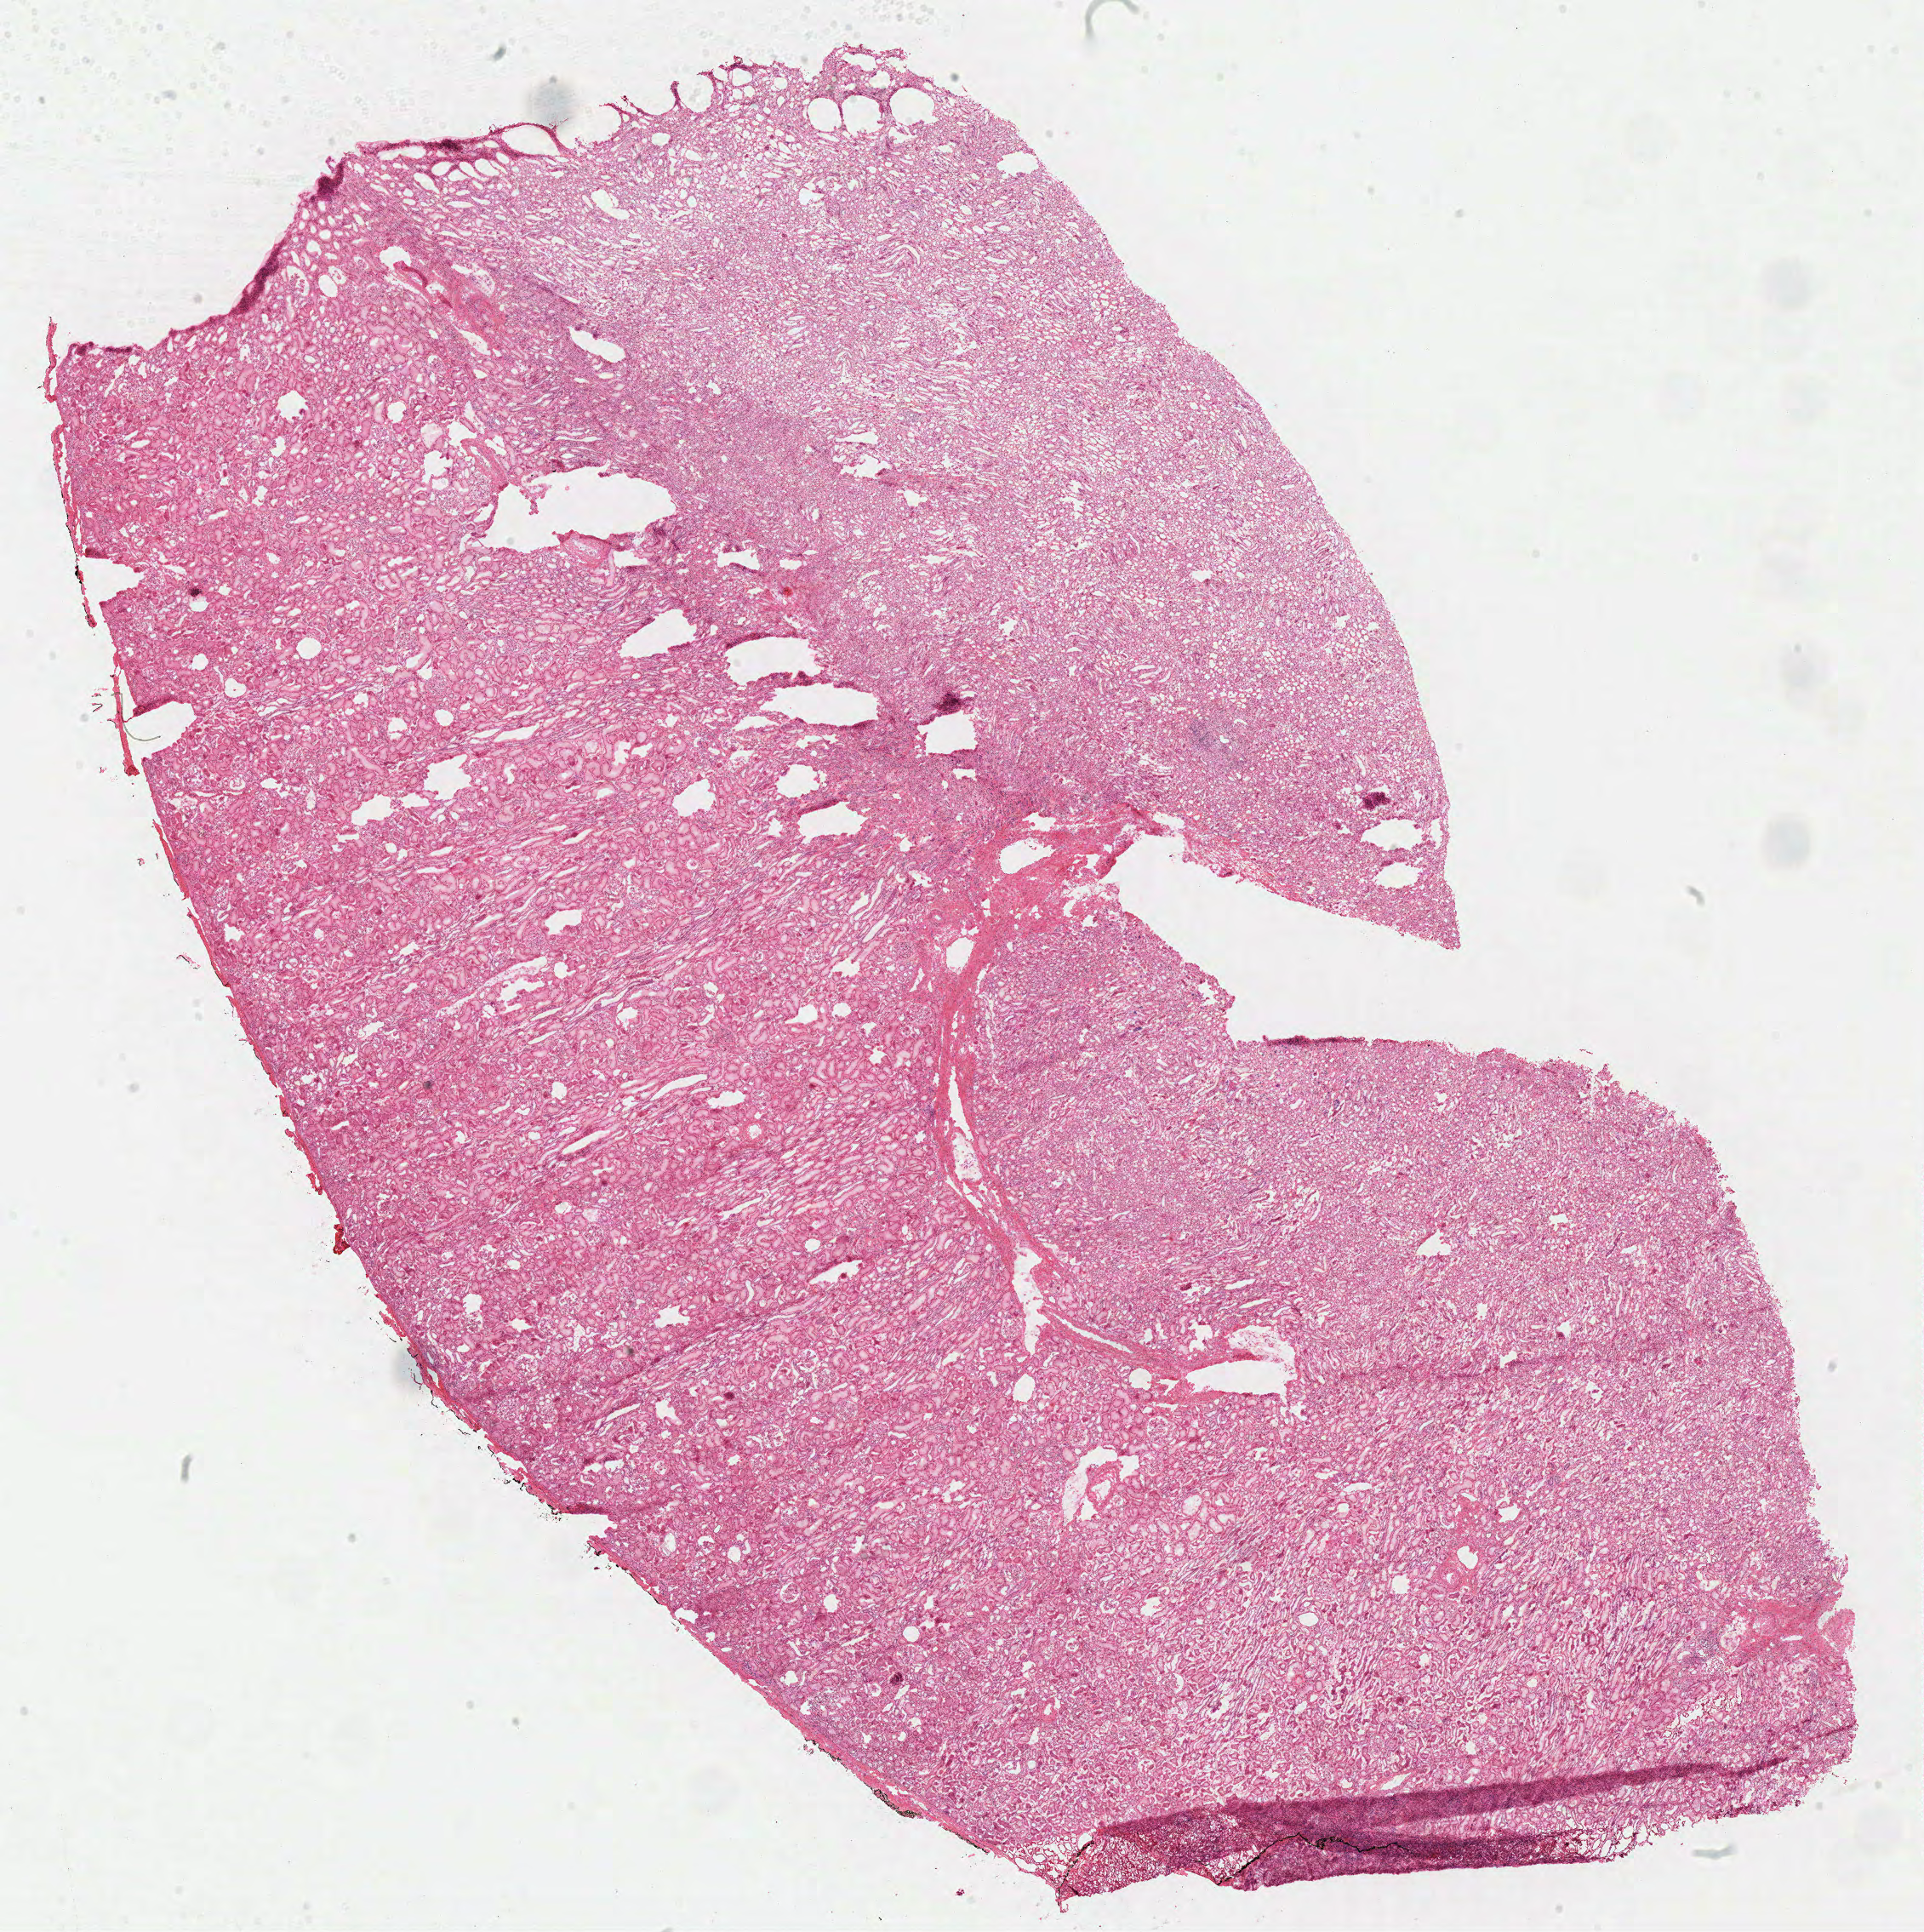
Digitized H&E-stained tissue section (whole slide), whole scanned area (about 17.8 x 17.9 mm, slide scanned at 40x) shown as a low-resolution overview; frozen section; solid tissue normal (non-tumour tissue) sample from the kidney. Female patient; age at initial diagnosis 57 years.
This section: solid tissue normal sample (biorepository sample class). Patient diagnosis: Papillary adenocarcinoma, NOS.